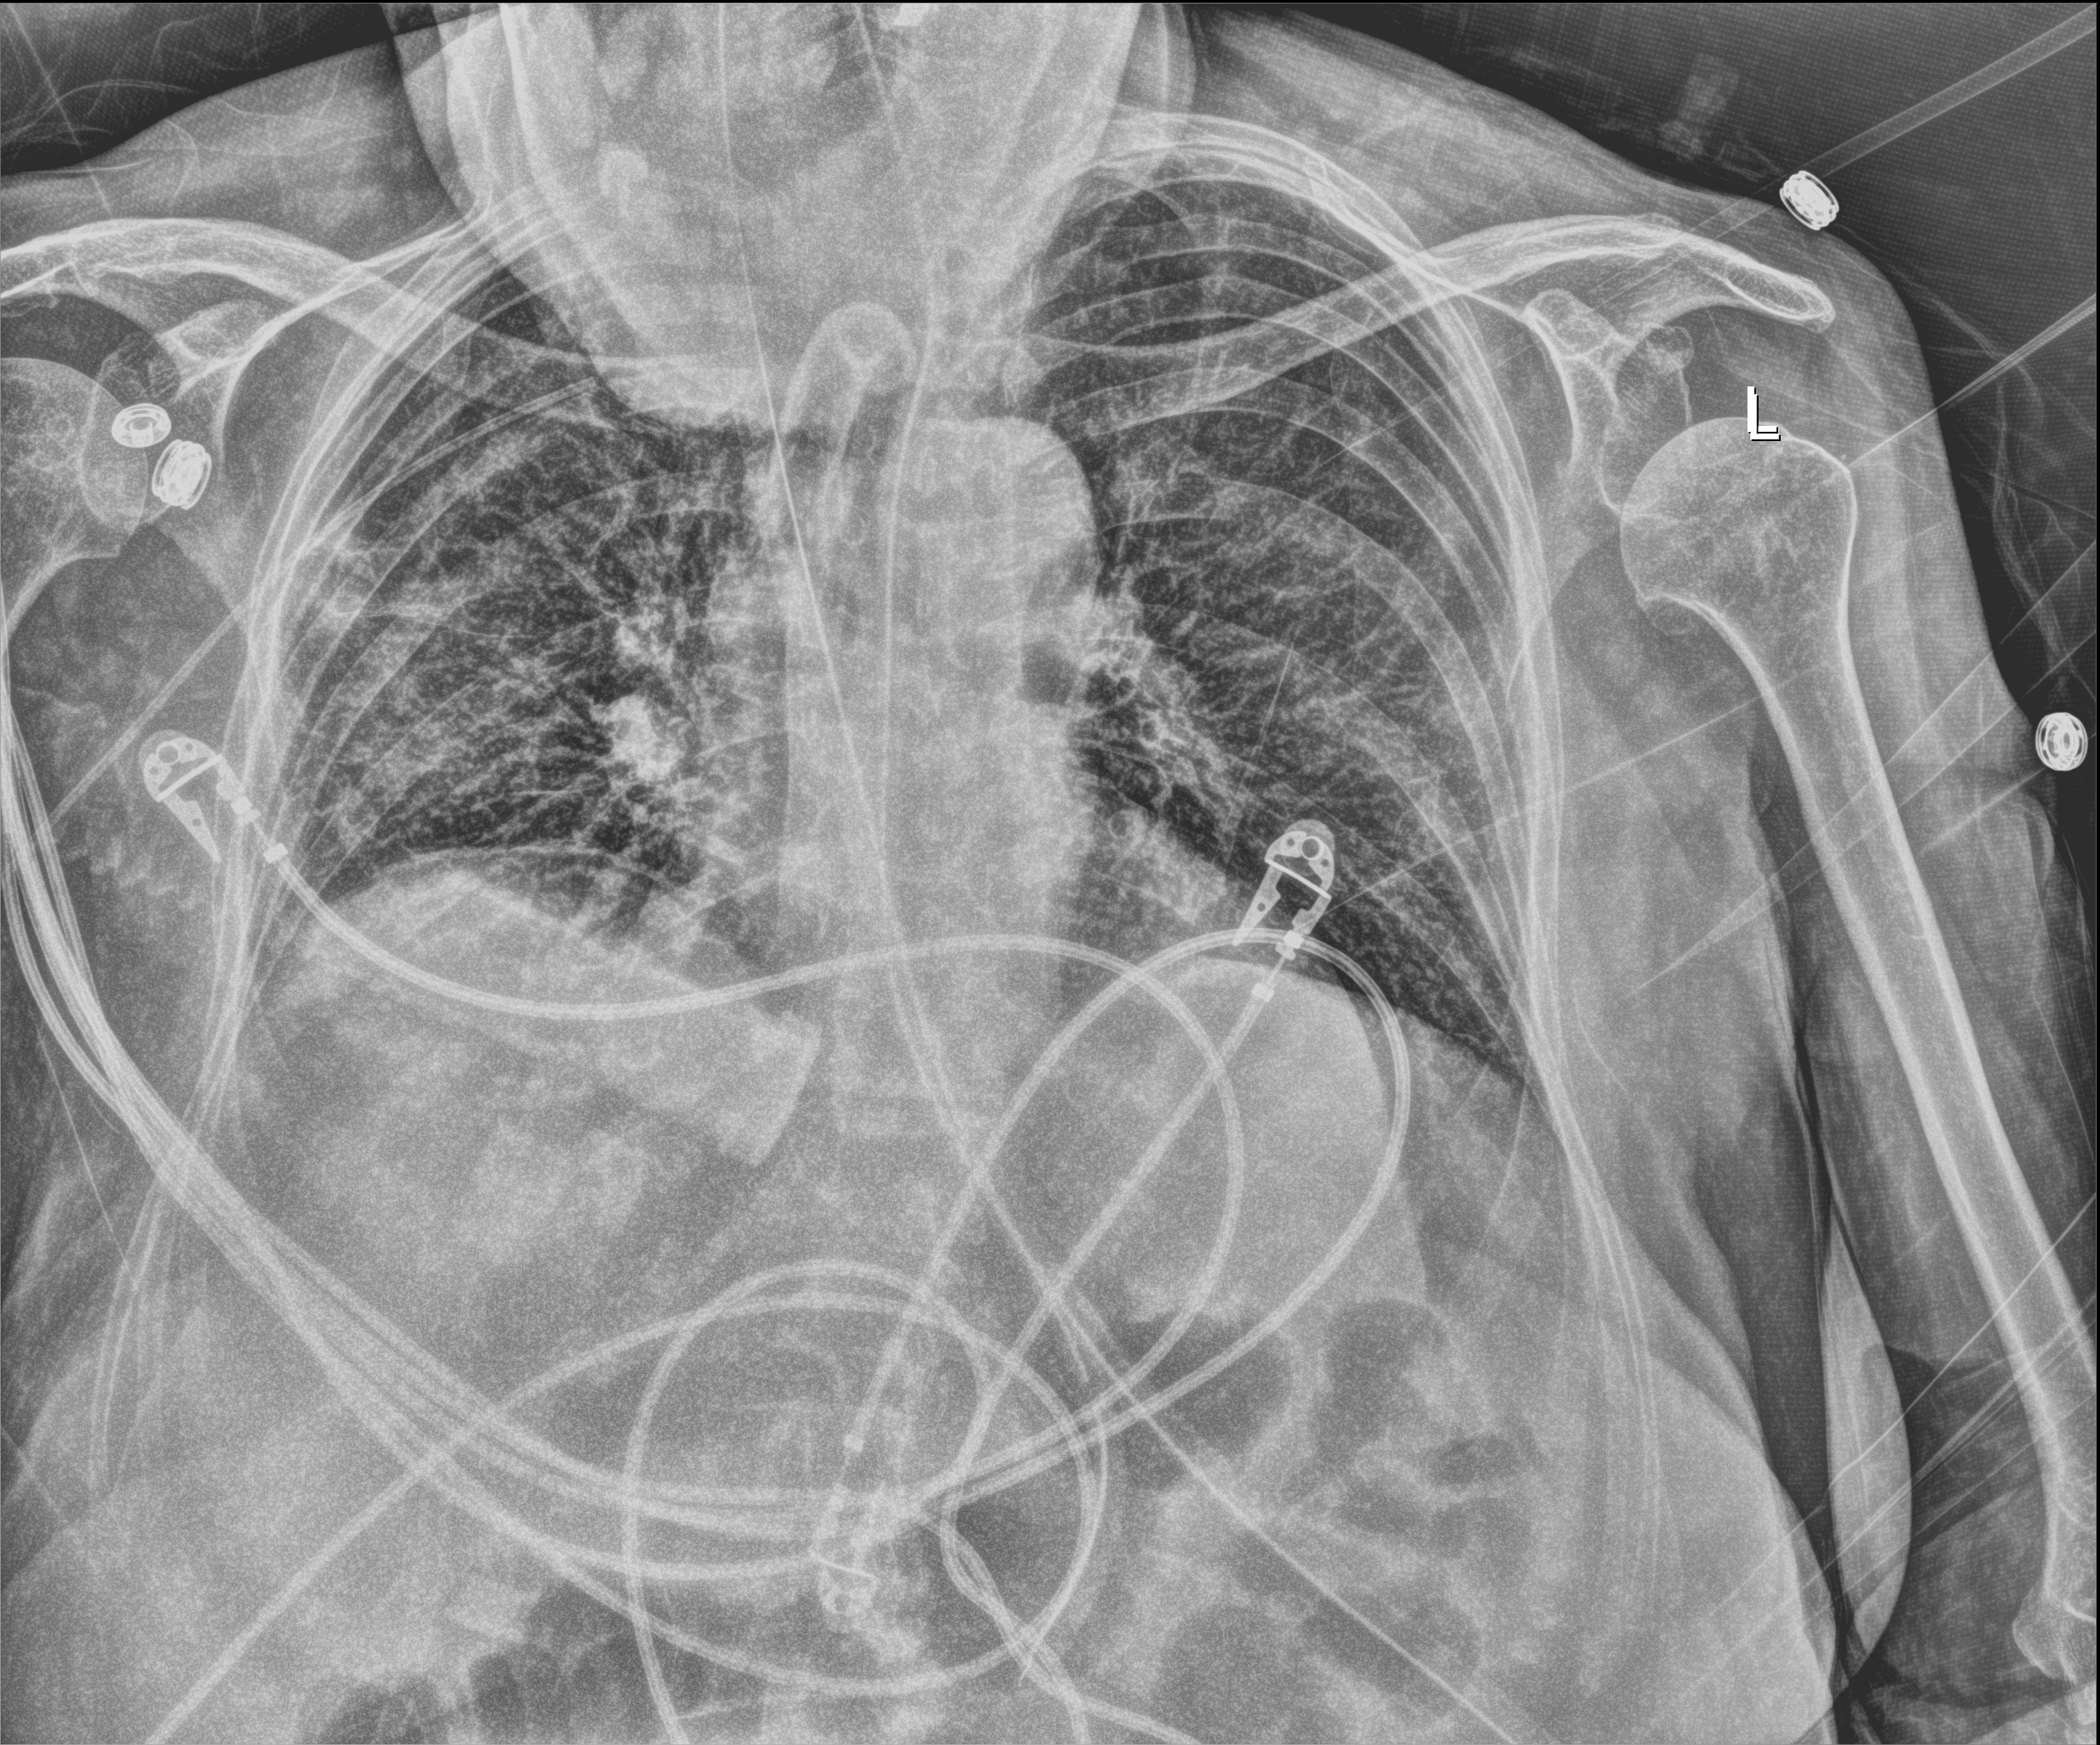
Chest radiograph, anteroposterior (AP) projection. Female patient hospitalised with COVID-19, age 75–90 years.
From the hospital-stay record, not from the radiograph (when in the stay this image was taken is not recorded): mechanically ventilated during this hospital stay: yes; length of hospital stay: 82 days.